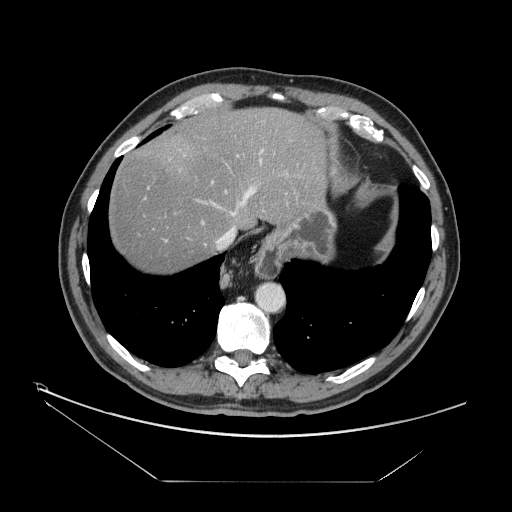
Contrast-enhanced abdominal CT, one axial slice; slice 134 of 161 in the series (ordered by position); reconstruction kernel STANDARD; 120 kVp; intravenous contrast given; soft-tissue window (W 400 / L 40 HU); 2.5 mm slice thickness; 512 × 512 image matrix. Male patient, age 65 years. From the clinical record (not read from this slice): diagnosis: colorectal cancer liver metastases, imaged before liver resection; multiple liver metastases: yes; largest metastasis: 4.2 cm; disease in both lobes: yes.
Annotated regions visible in this slice (expert manual segmentation):
- hepatic veins: bounding box <204,179,260,250> (left, top, right, bottom; pixels)
- liver: <108,108,325,272>
- planned liver remnant (the part of the liver to remain after resection): <108,108,325,272>
- portal vein (with intrahepatic branches): <145,120,265,242>